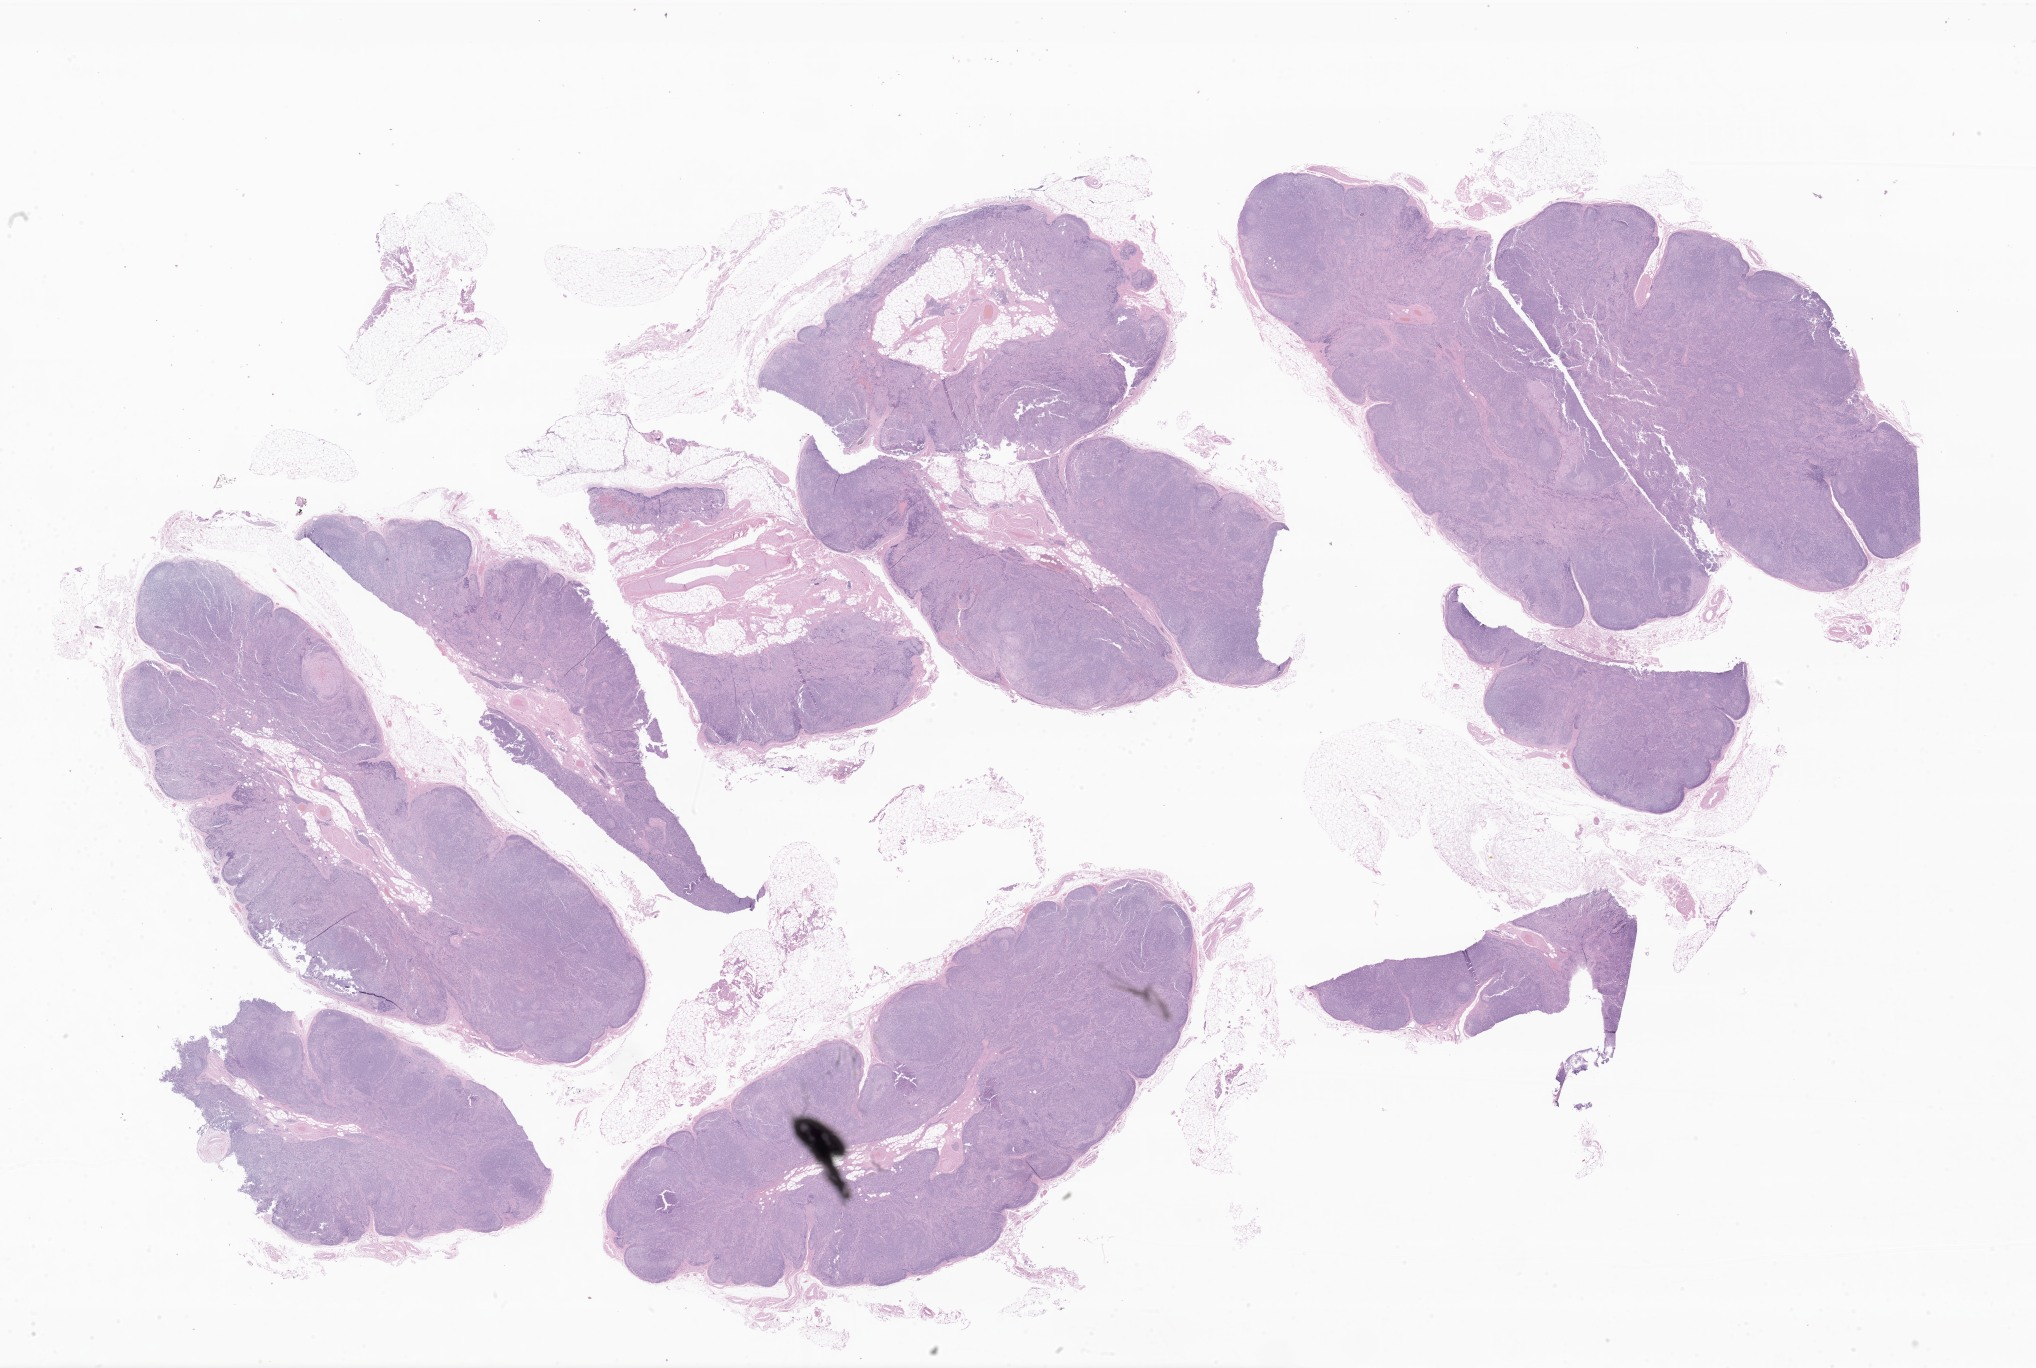
Digitized haematoxylin and eosin-stained section of tumor tissue from the skin of lower limb — low-resolution overview of the scanned area, about 34.3 x 23.1 mm, formalin-fixed, paraffin-embedded (FFPE) tissue. Patient: male, age 163 months (13 years 7 months).
* recorded diagnosis: Malignant melanoma, NOS